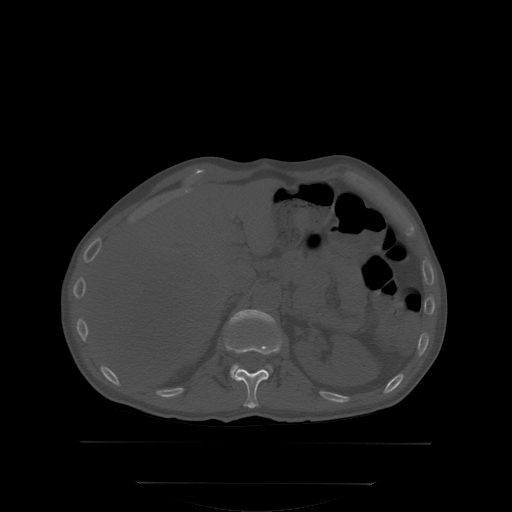
CT including the spine, one axial slice; position 163 of 350 along the scan axis; bone window (W 1800 / L 400 HU); 512 × 512 image matrix, field of view 500 × 500 mm. Patient: male, 58 years. Case-level facts recorded for this patient, not image findings: primary cancer: prostate.
Structures marked on this image (semi-automatic segmentation, software-assisted and operator-edited):
- L1 vertebra: bounding box <229,310,276,378> (left, top, right, bottom; pixels)
- T12 vertebra: <224,329,282,408>